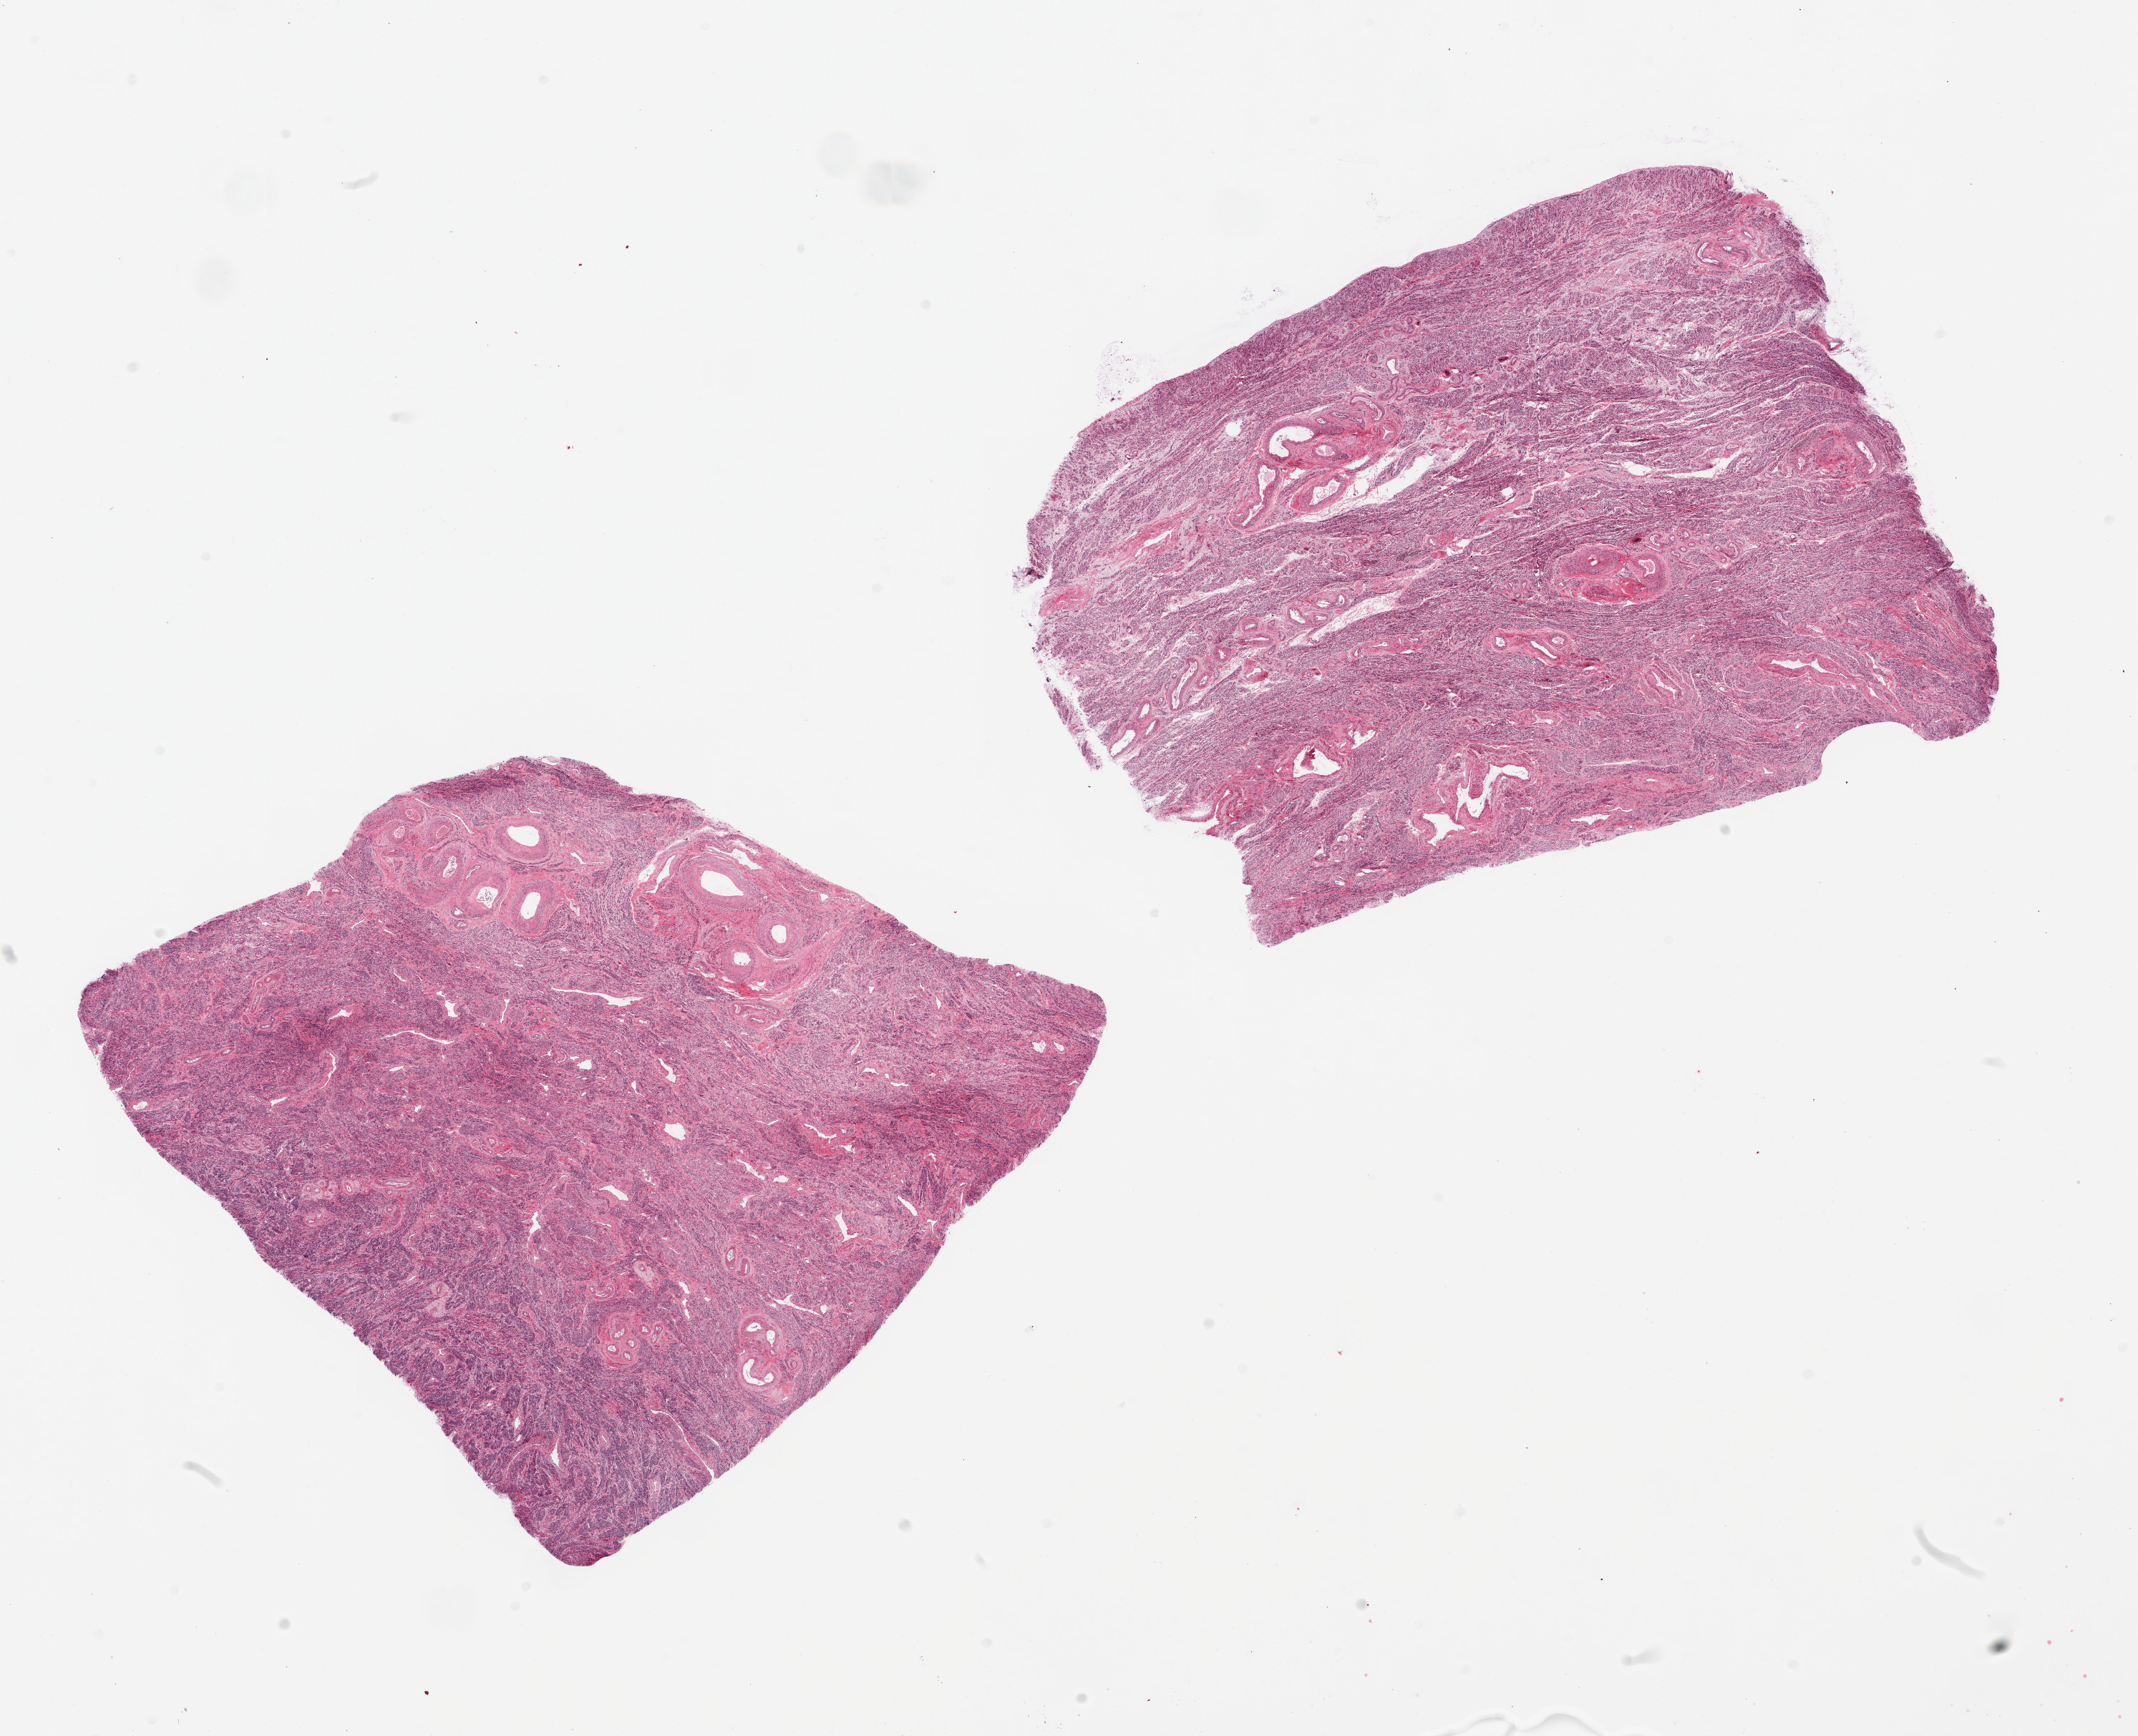
Digitized hematoxylin and eosin (H&E)-stained section, brightfield — whole scanned area (about 23.6 x 19.2 mm) shown as a low-resolution overview, PAXgene-fixed paraffin-embedded (PFPE) section, target tissue: ovary, tissue donor sample.
Pathologist's review note for this sample: 2 pieces; atrophic, no corpora.